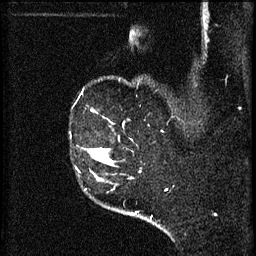
Breast MRI (dynamic contrast-enhanced), one sagittal slice; position 49 of 60 along the scan axis; 3 images stored at this slice position (order not interpretable as contrast timing); 1.5 T; TE 4.2 ms, TR 8.2 ms; 256 × 256 image matrix, field of view 180 × 180 mm. Female patient, age 49 years.
Structures marked on this image (semi-automatic segmentation, software-assisted and operator-edited):
- analysis volume of interest (the breast-tissue region the enhancement analysis was run in; not a lesion): bounding box (x1, y1, x2, y2) in pixels: (89, 148, 105, 163)
- tumour enhancement mask (voxels above the 70 % enhancement threshold inside the analysis volume of interest): (89, 150, 105, 163)